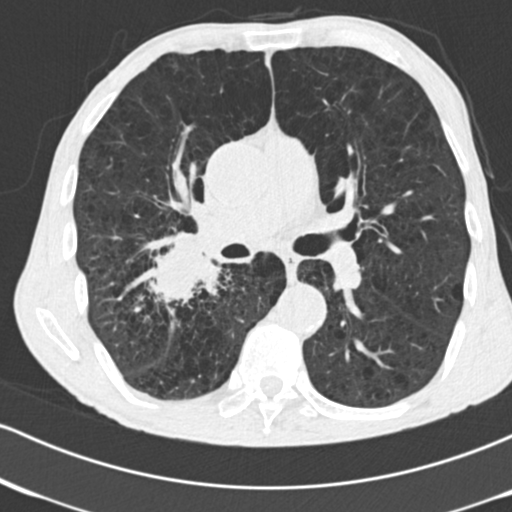
Chest CT (low-dose screening protocol), one axial image; second annual screen; lung window (W 1500 / L -600 HU); 2 mm slice thickness. Male, age 64 years at enrolment. Current smoker at enrolment.
Lesion marked by an expert reader, bounding box <132,231,238,328> (left, top, right, bottom; pixels). The exam's reader record, not a measurement of the box and not confirmed to be the same lesion: non-calcified nodule or mass ≥4 mm, 52 × 37 mm, spiculated (stellate) margins, soft tissue attenuation, pre-existing on the prior screen: no. Official screen result: positive, other. Lung cancer was diagnosed 28 days after this screen: adenocarcinoma, NOS, right lower lobe, stage IV (AJCC 6th edition), 60 mm at pathology.